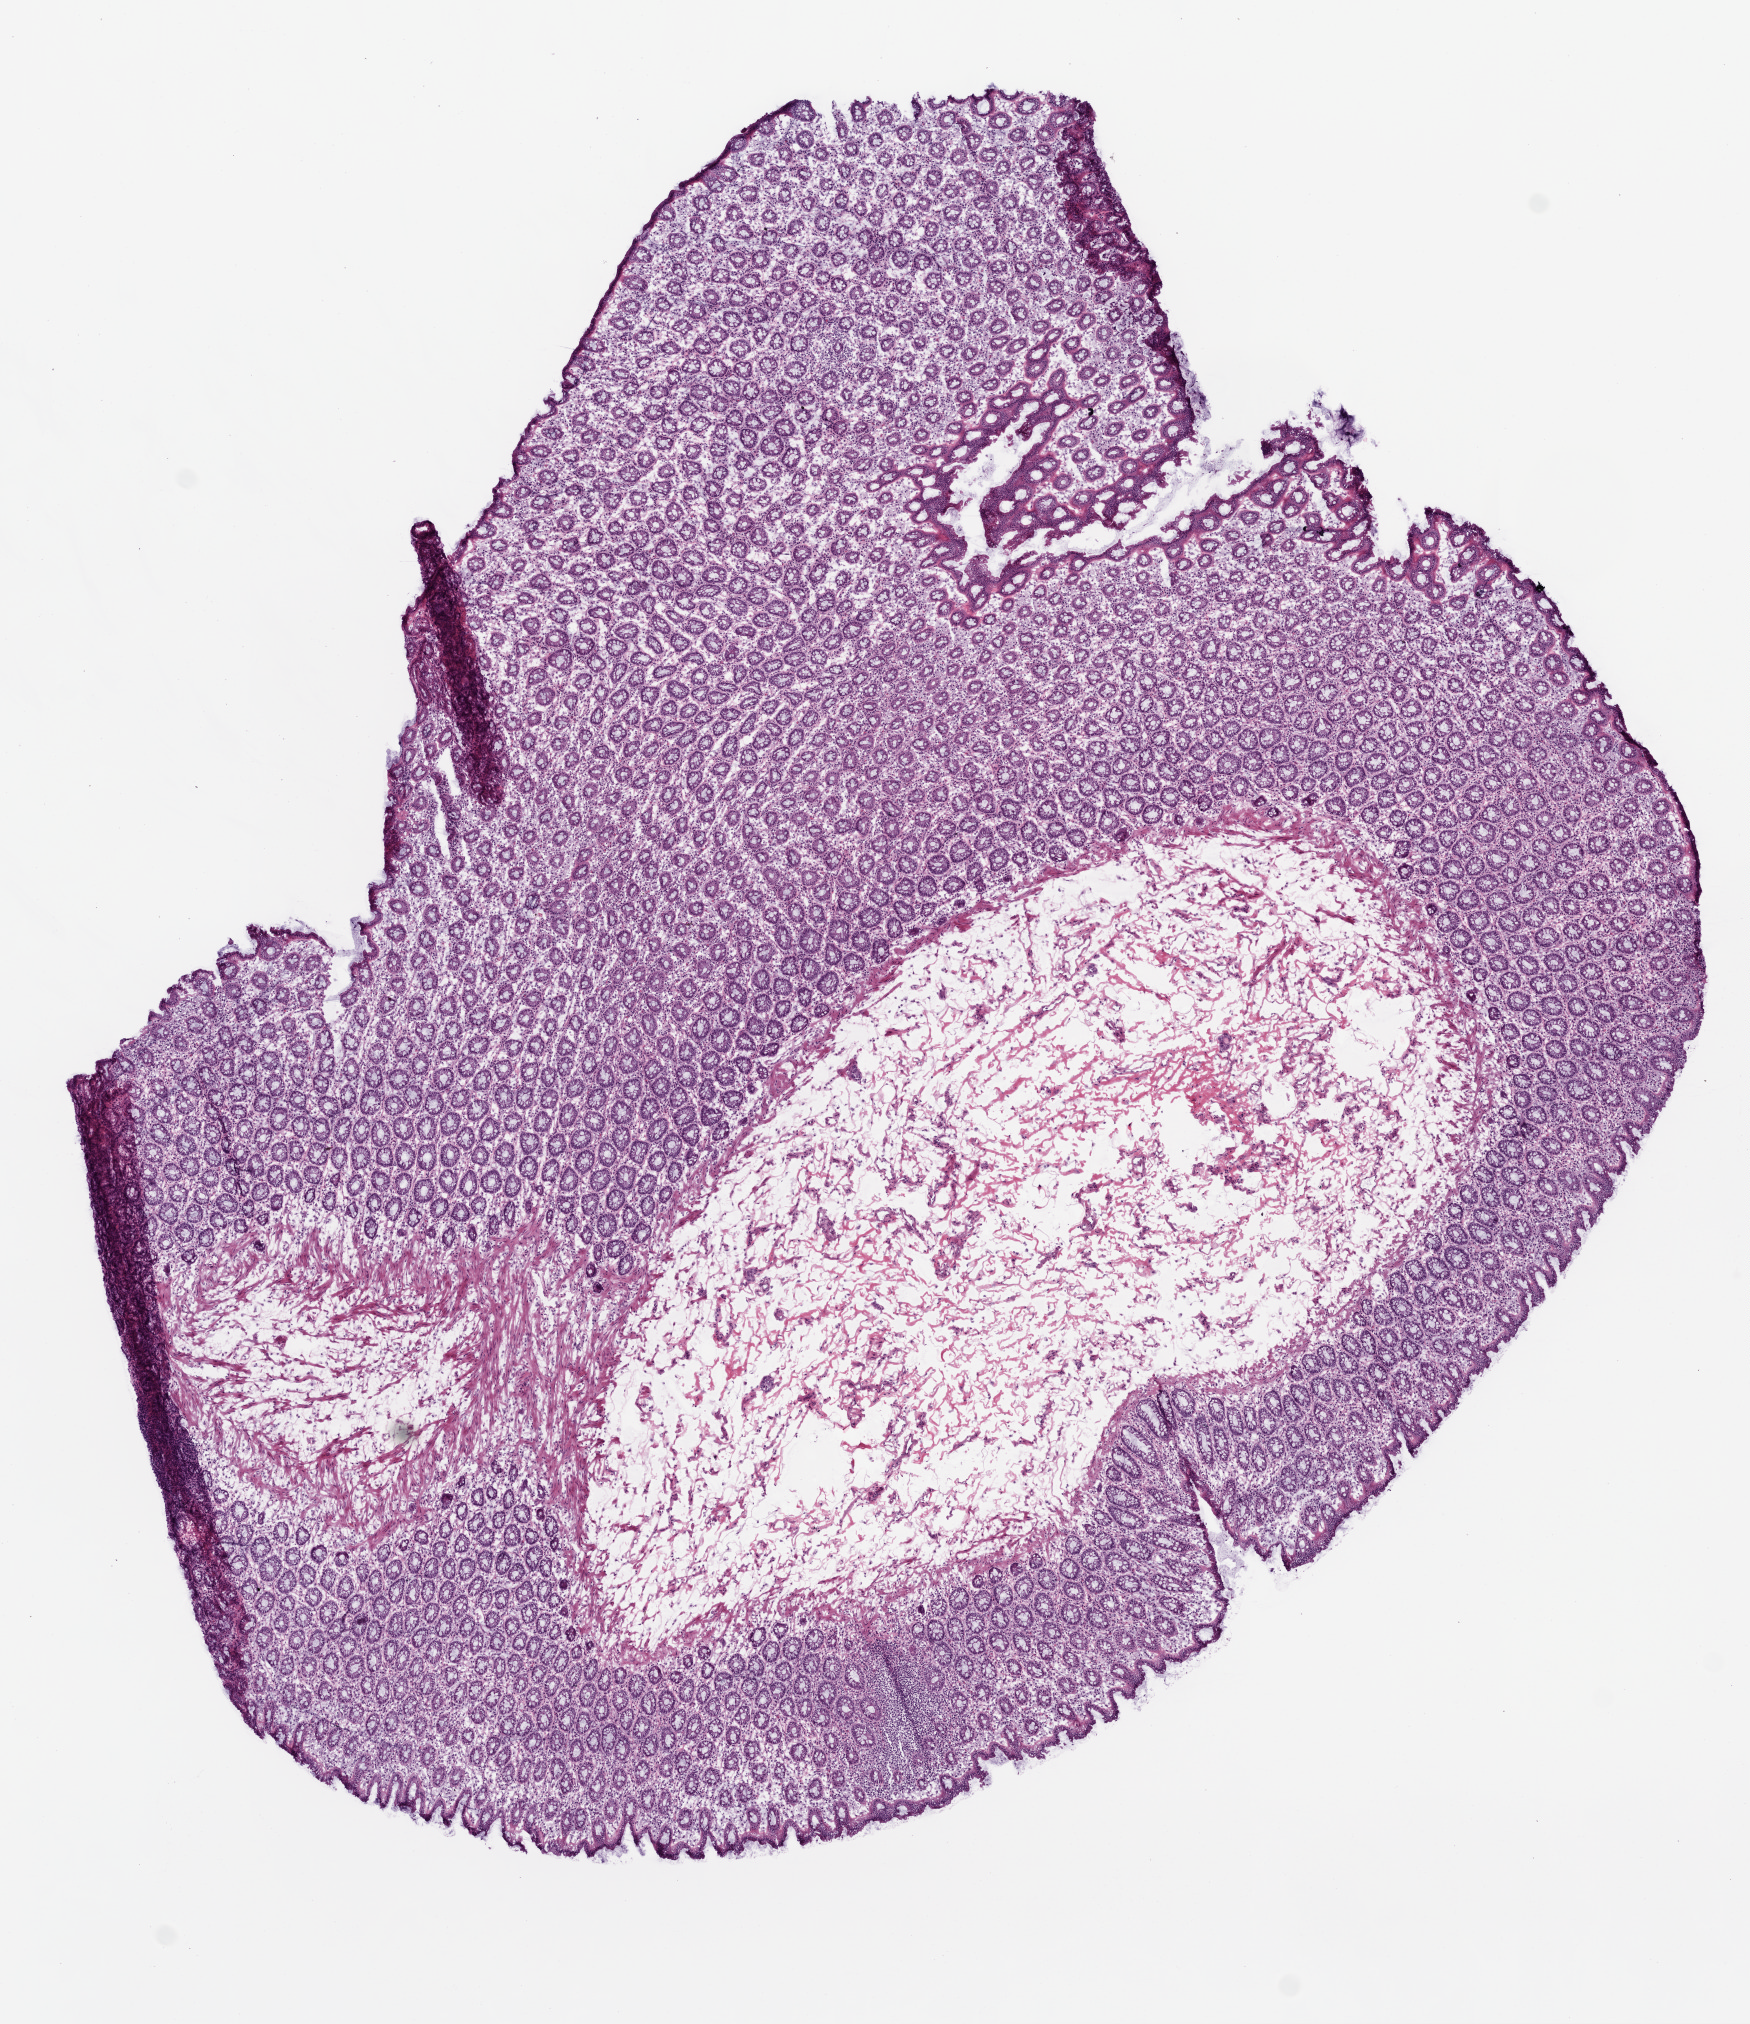
Digitized H&E tissue section (whole slide) — low-resolution overview of the scanned area, about 7.0 x 8.1 mm; frozen section from the top of the tissue portion; sample: solid tissue normal (non-tumour tissue), colon. Patient: male, age at initial diagnosis 63 years.
This section: solid tissue normal (non-tumour) sample from the same patient. Patient diagnosis: Adenocarcinoma, NOS.